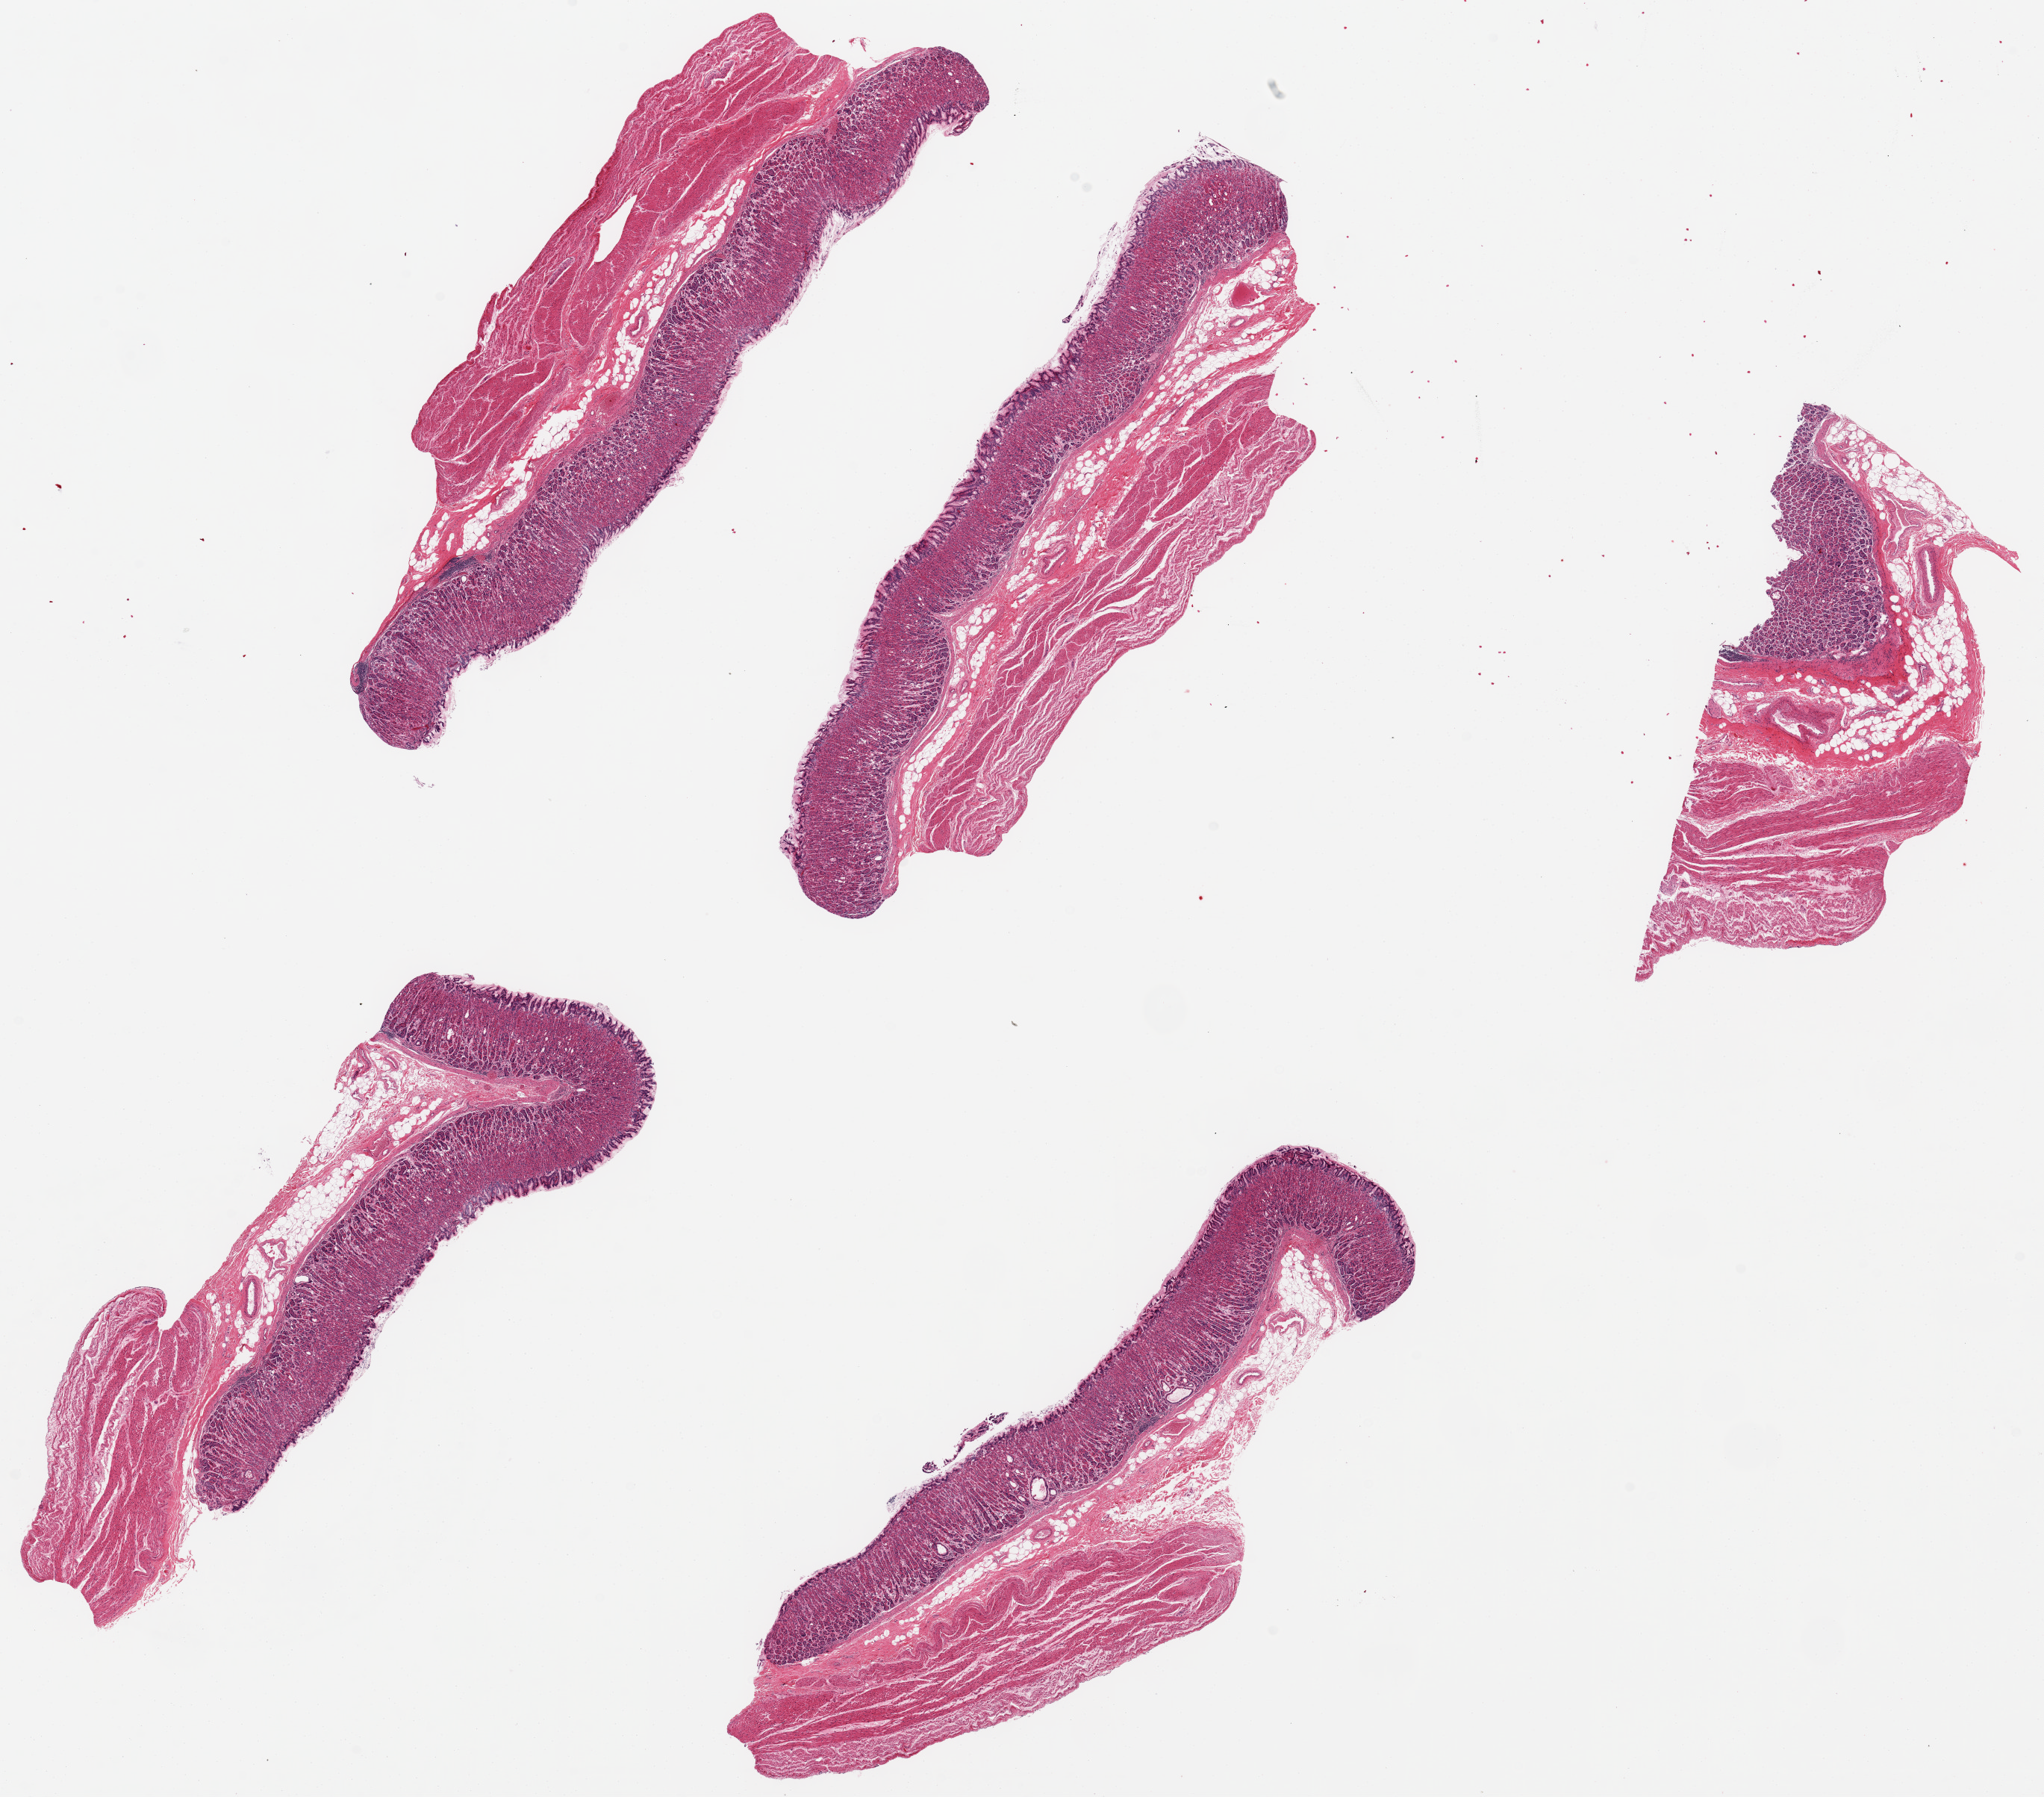
H&E whole-slide image — low-resolution overview of the scanned area, about 21.7 x 19.0 mm, PAXgene-fixed paraffin-embedded (PFPE) section, sampled site (target tissue): stomach, donor tissue sample. Male donor.
Pathologist's review note for this sample: 6 8x2.5mm pieces; mucosa well preserved generally, 20-30% of thickness.